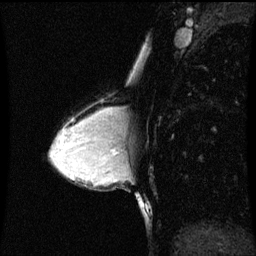
Breast MRI (dynamic contrast-enhanced), one sagittal slice. Slice 37 of 60 in the series (ordered by position). Dynamic contrast-enhanced series, image 2 of 3 at this slice position (ordered by acquisition). 1.5 T. TE 4.2 ms, TR 8.9 ms. 2 mm slice thickness. 256 × 256 image matrix, field of view 200 × 200 mm. Patient: female, 33 years. From the clinical record (not read from this slice): setting: breast cancer imaged before/during neoadjuvant chemotherapy; receptor status: HER2-positive.
Annotated regions visible in this slice (semi-automatic segmentation, software-assisted and operator-edited):
- analysis volume of interest (the breast-tissue region the enhancement analysis was run in; not a lesion): bounding box <107,108,118,147> (left, top, right, bottom; pixels)
- tumour enhancement mask (voxels above the 70 % enhancement threshold inside the analysis volume of interest): <107,108,116,117>